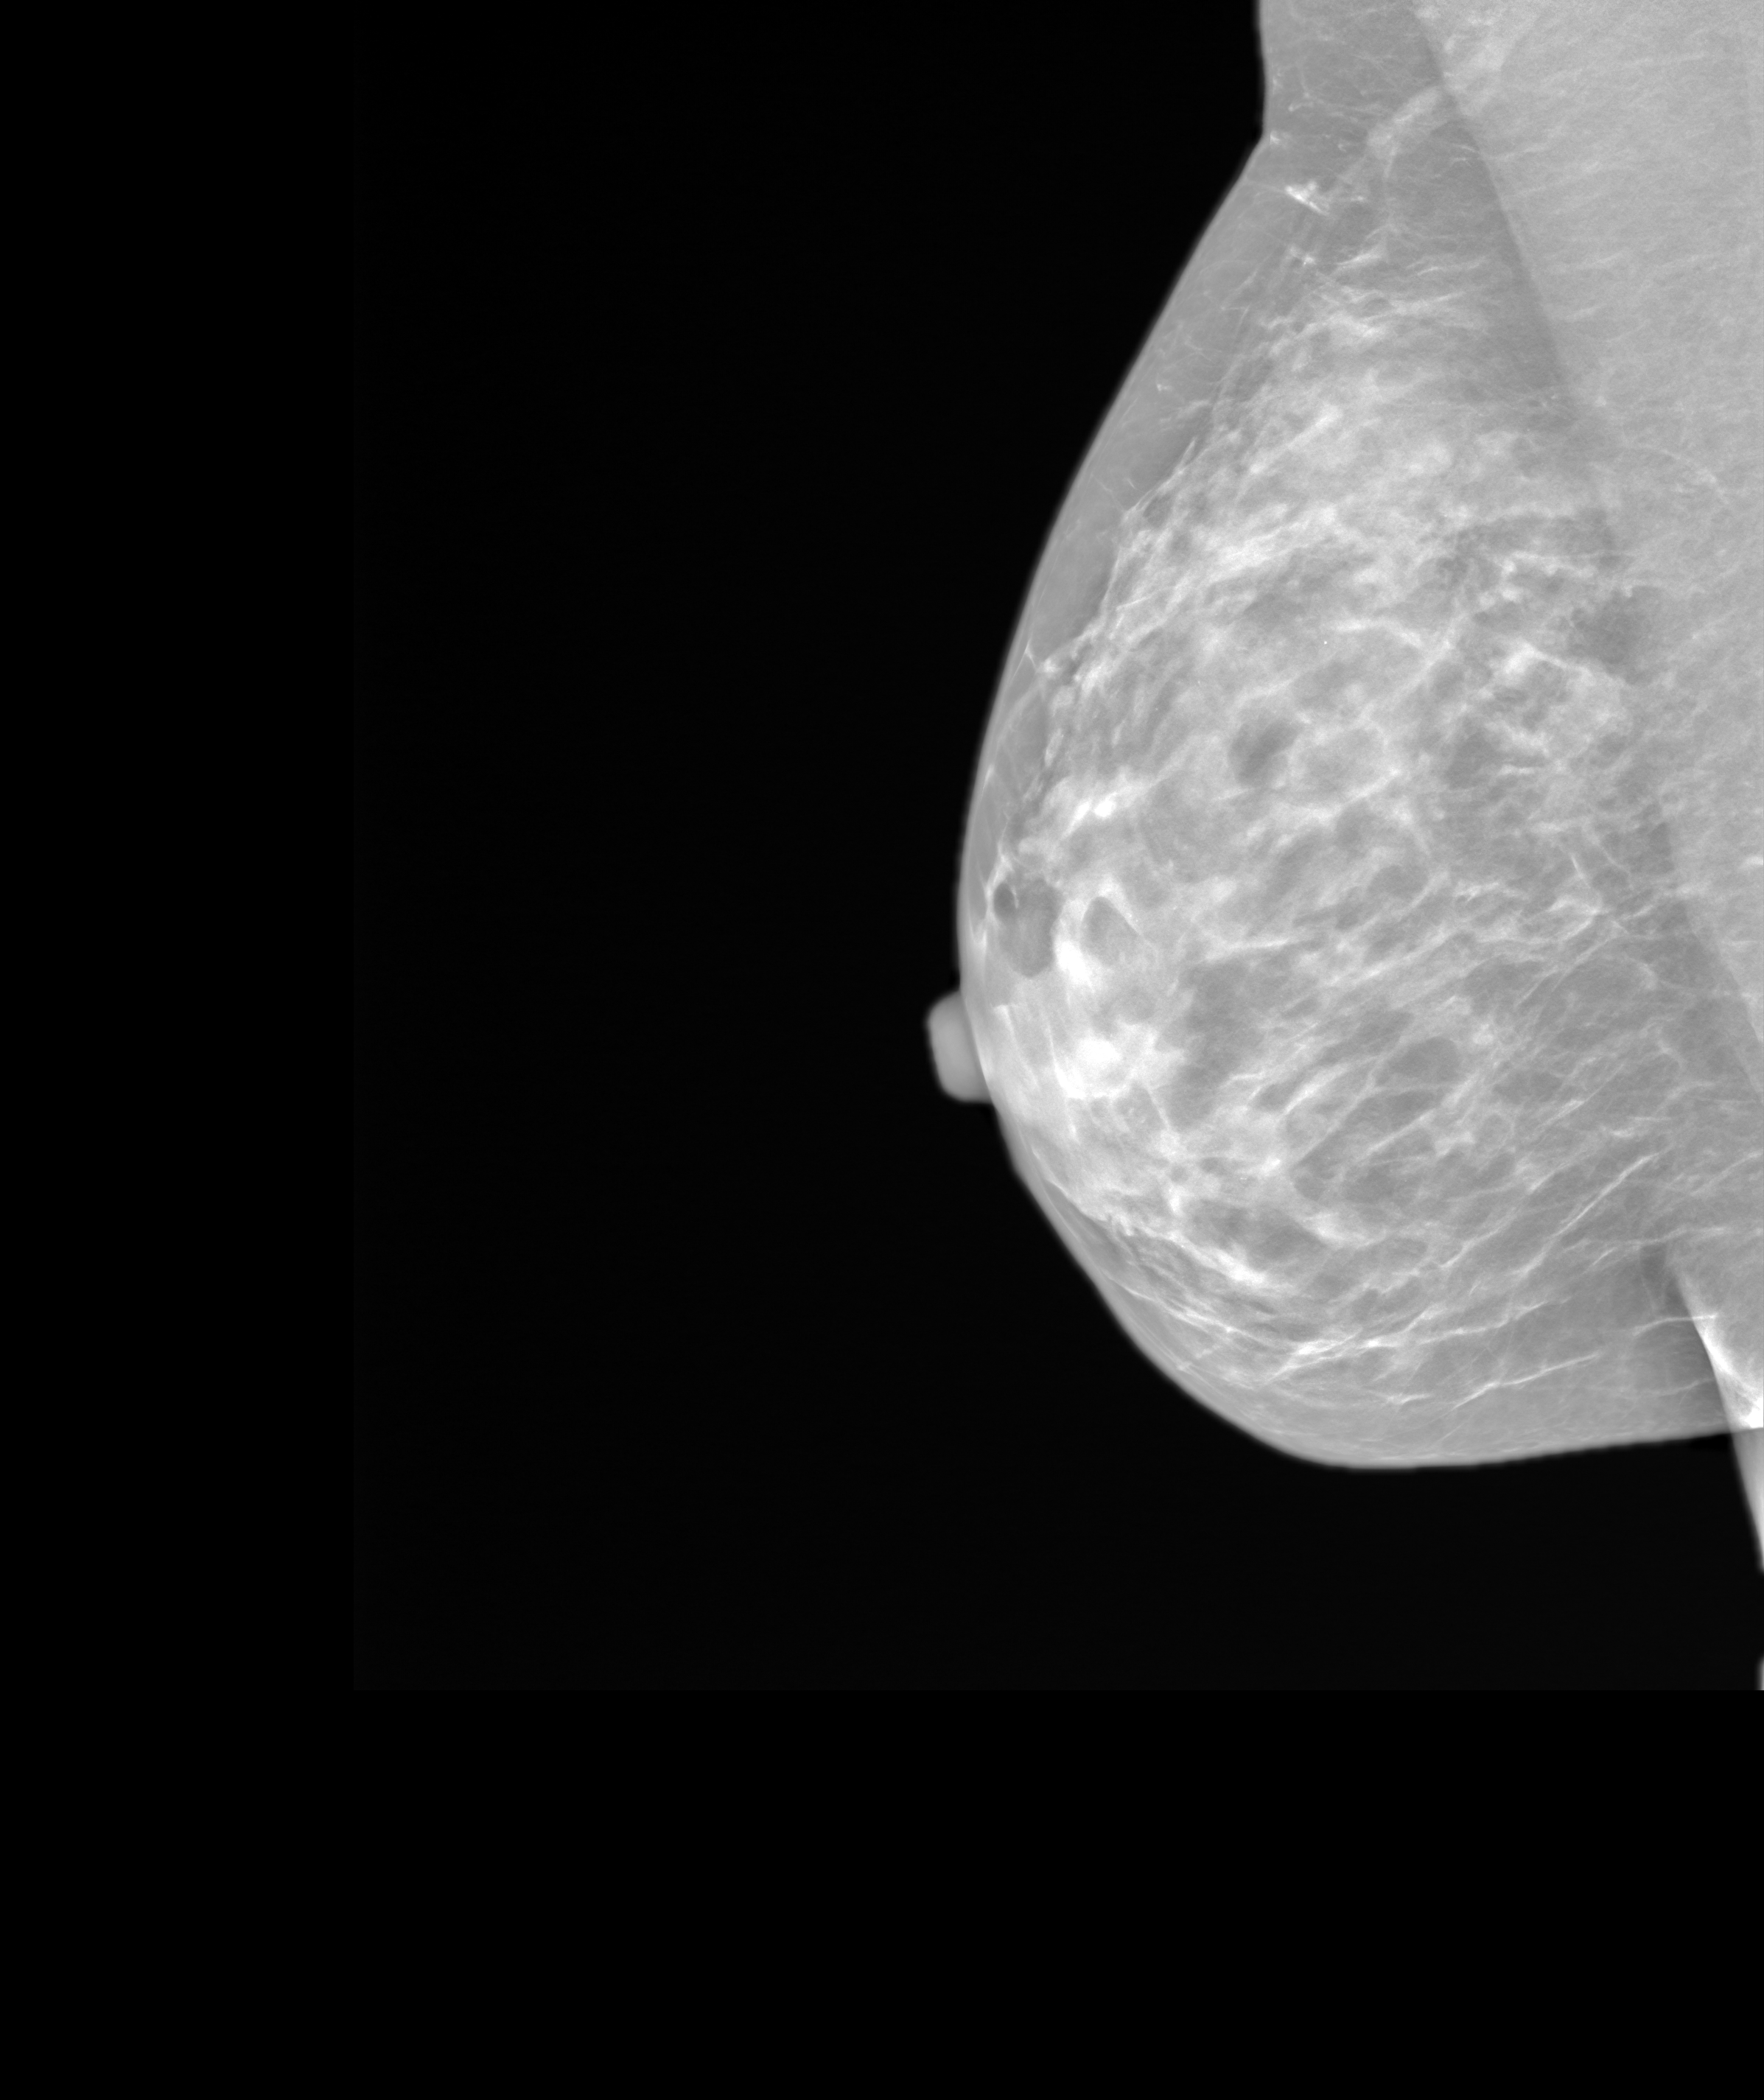
Screening examination. Patient aged 48 years (female).
Image type: synthesized 2-D view from tomosynthesis. Breast: right. Projection: MLO view.